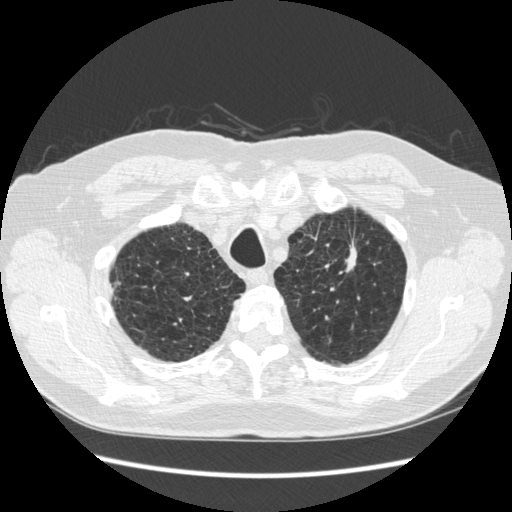
Low-dose screening chest CT, one axial slice; slice 228 of 267 in the series (ordered by position); reconstruction kernel STANDARD; 120 kVp; lung window (W 1500 / L -600 HU); 1.25 mm slice thickness; 512 × 512 image matrix, field of view 360 × 360 mm.
Annotated regions visible in this slice (expert manual segmentation):
- lesion 1 (tumor, upper lobe of left lung): box from (x=346, y=243) to (x=357, y=268) px